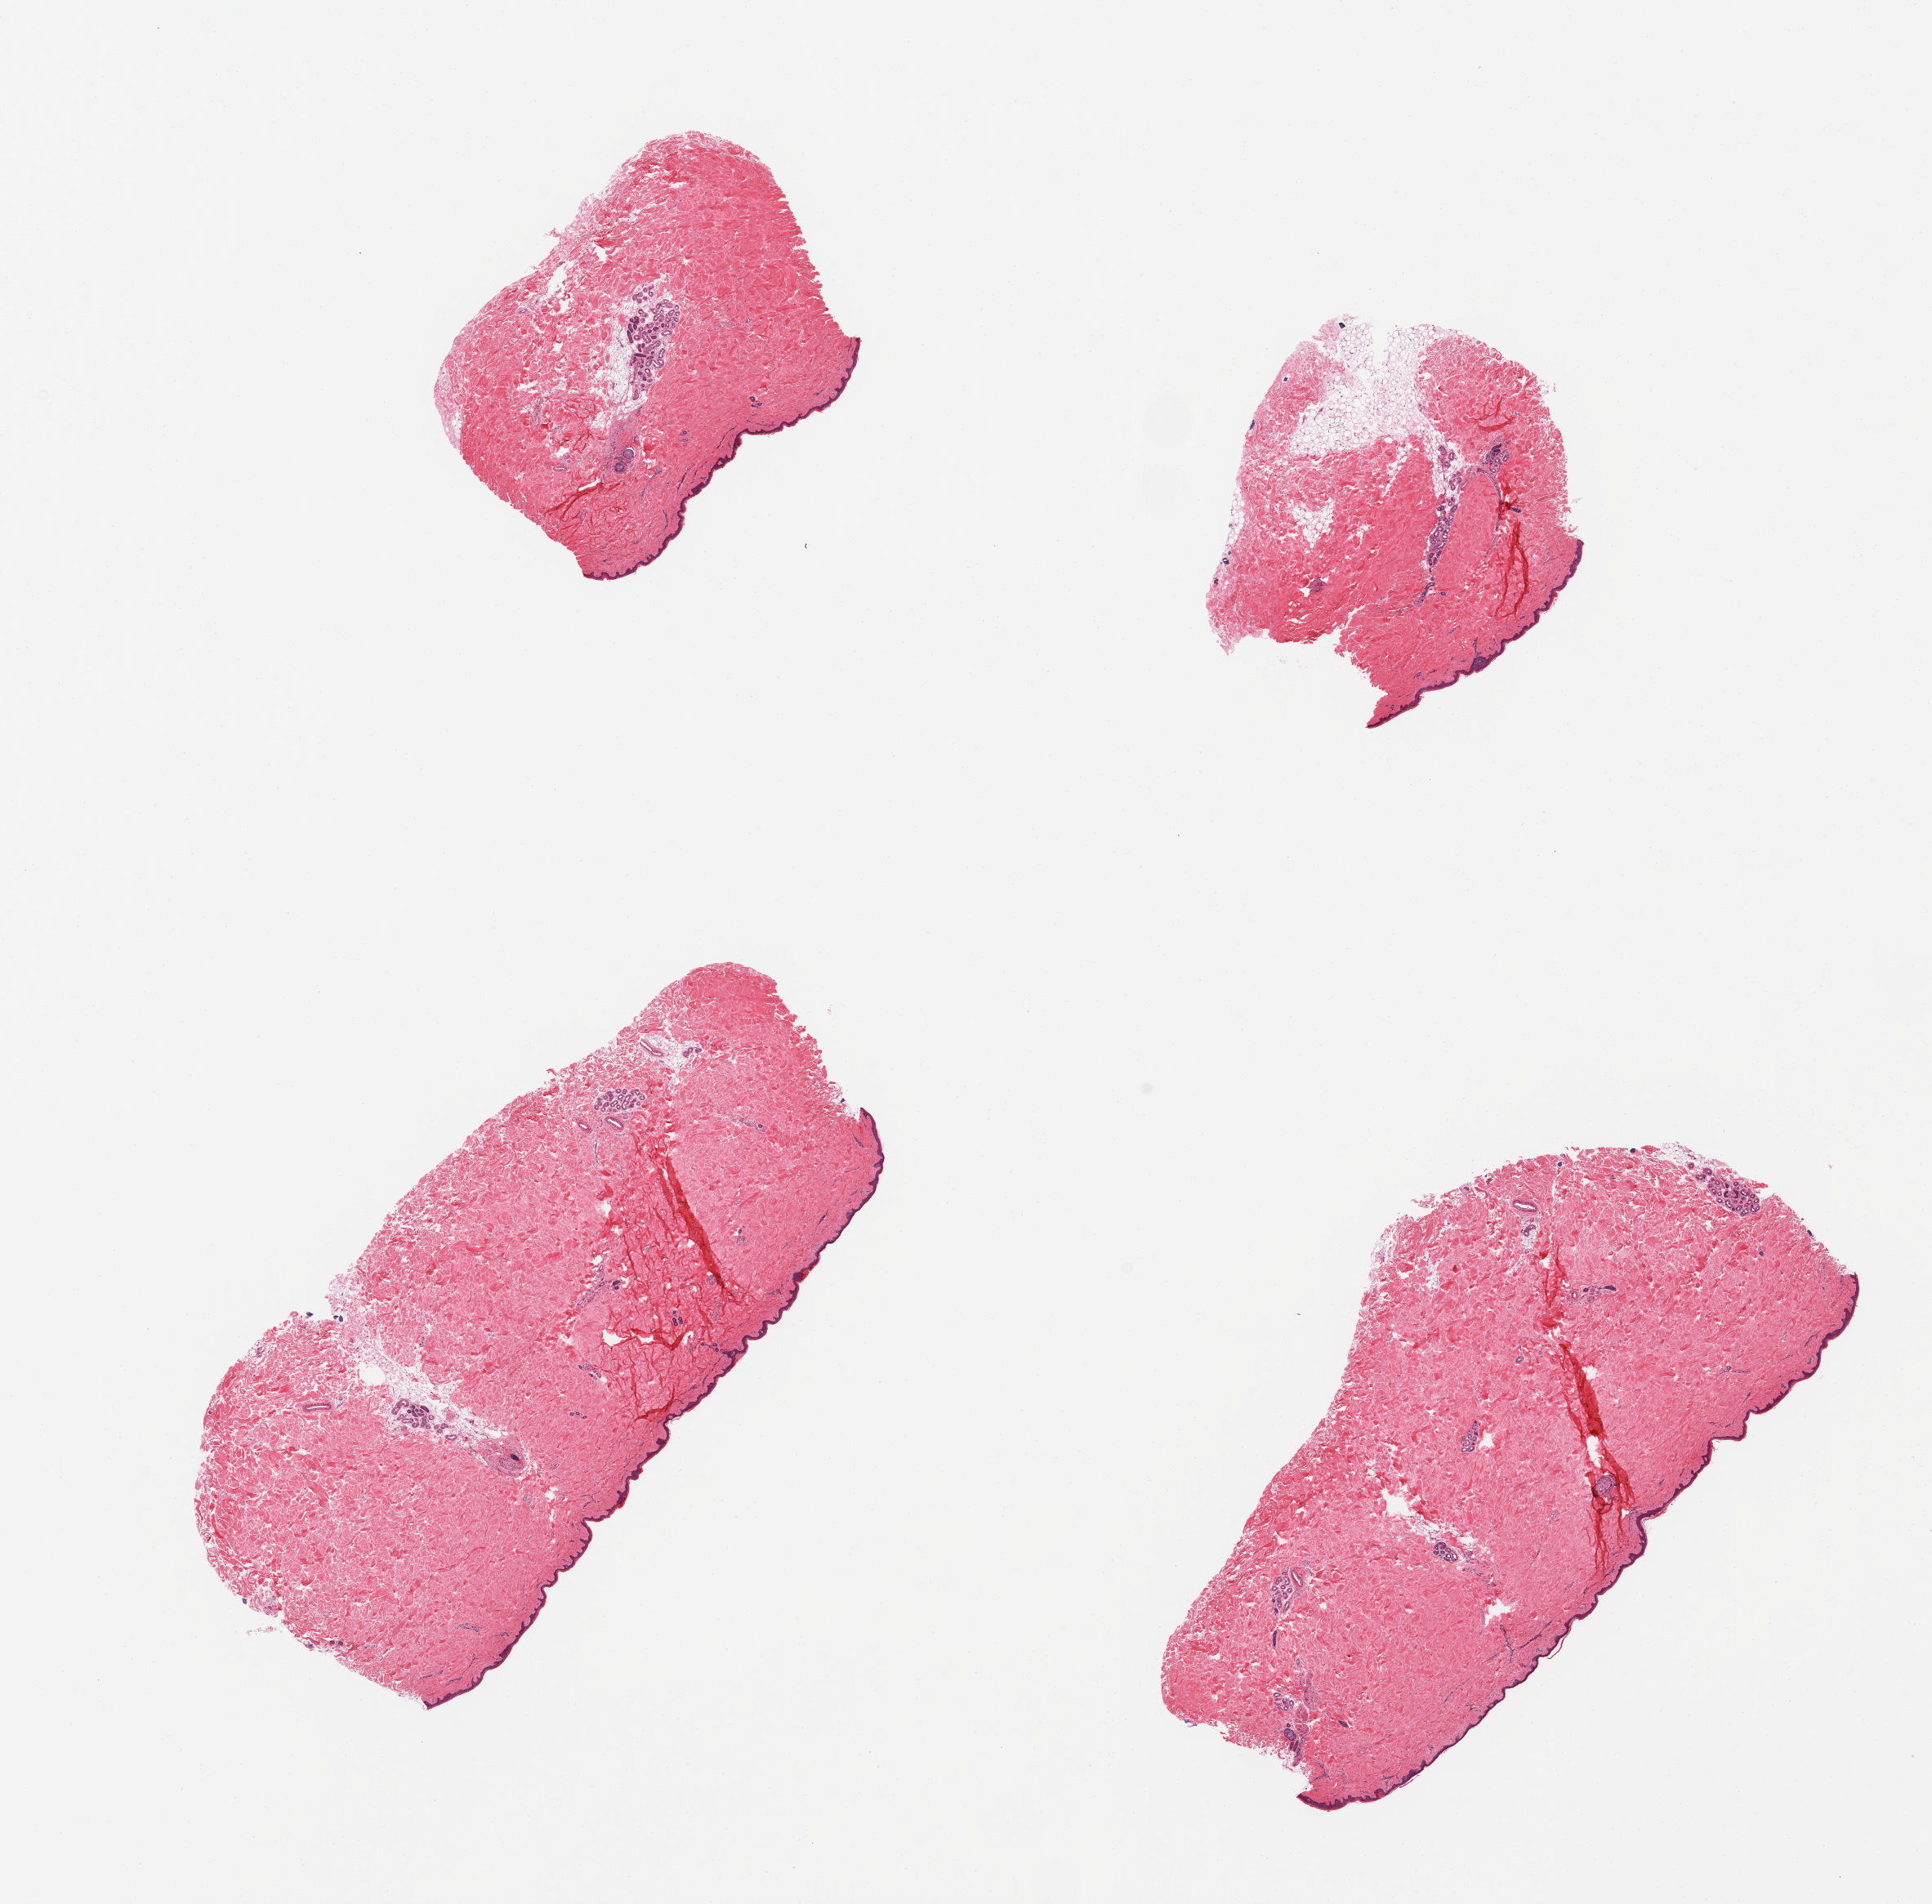
Haematoxylin and eosin whole-slide image, brightfield, low-resolution overview of the scanned area, about 18.7 x 18.4 mm; PAXgene-fixed, paraffin-embedded tissue; target tissue: skin of suprapubic region; tissue donor sample. Male donor.
- reviewer comment on this tissue sample: 4 pieces; well trimmed